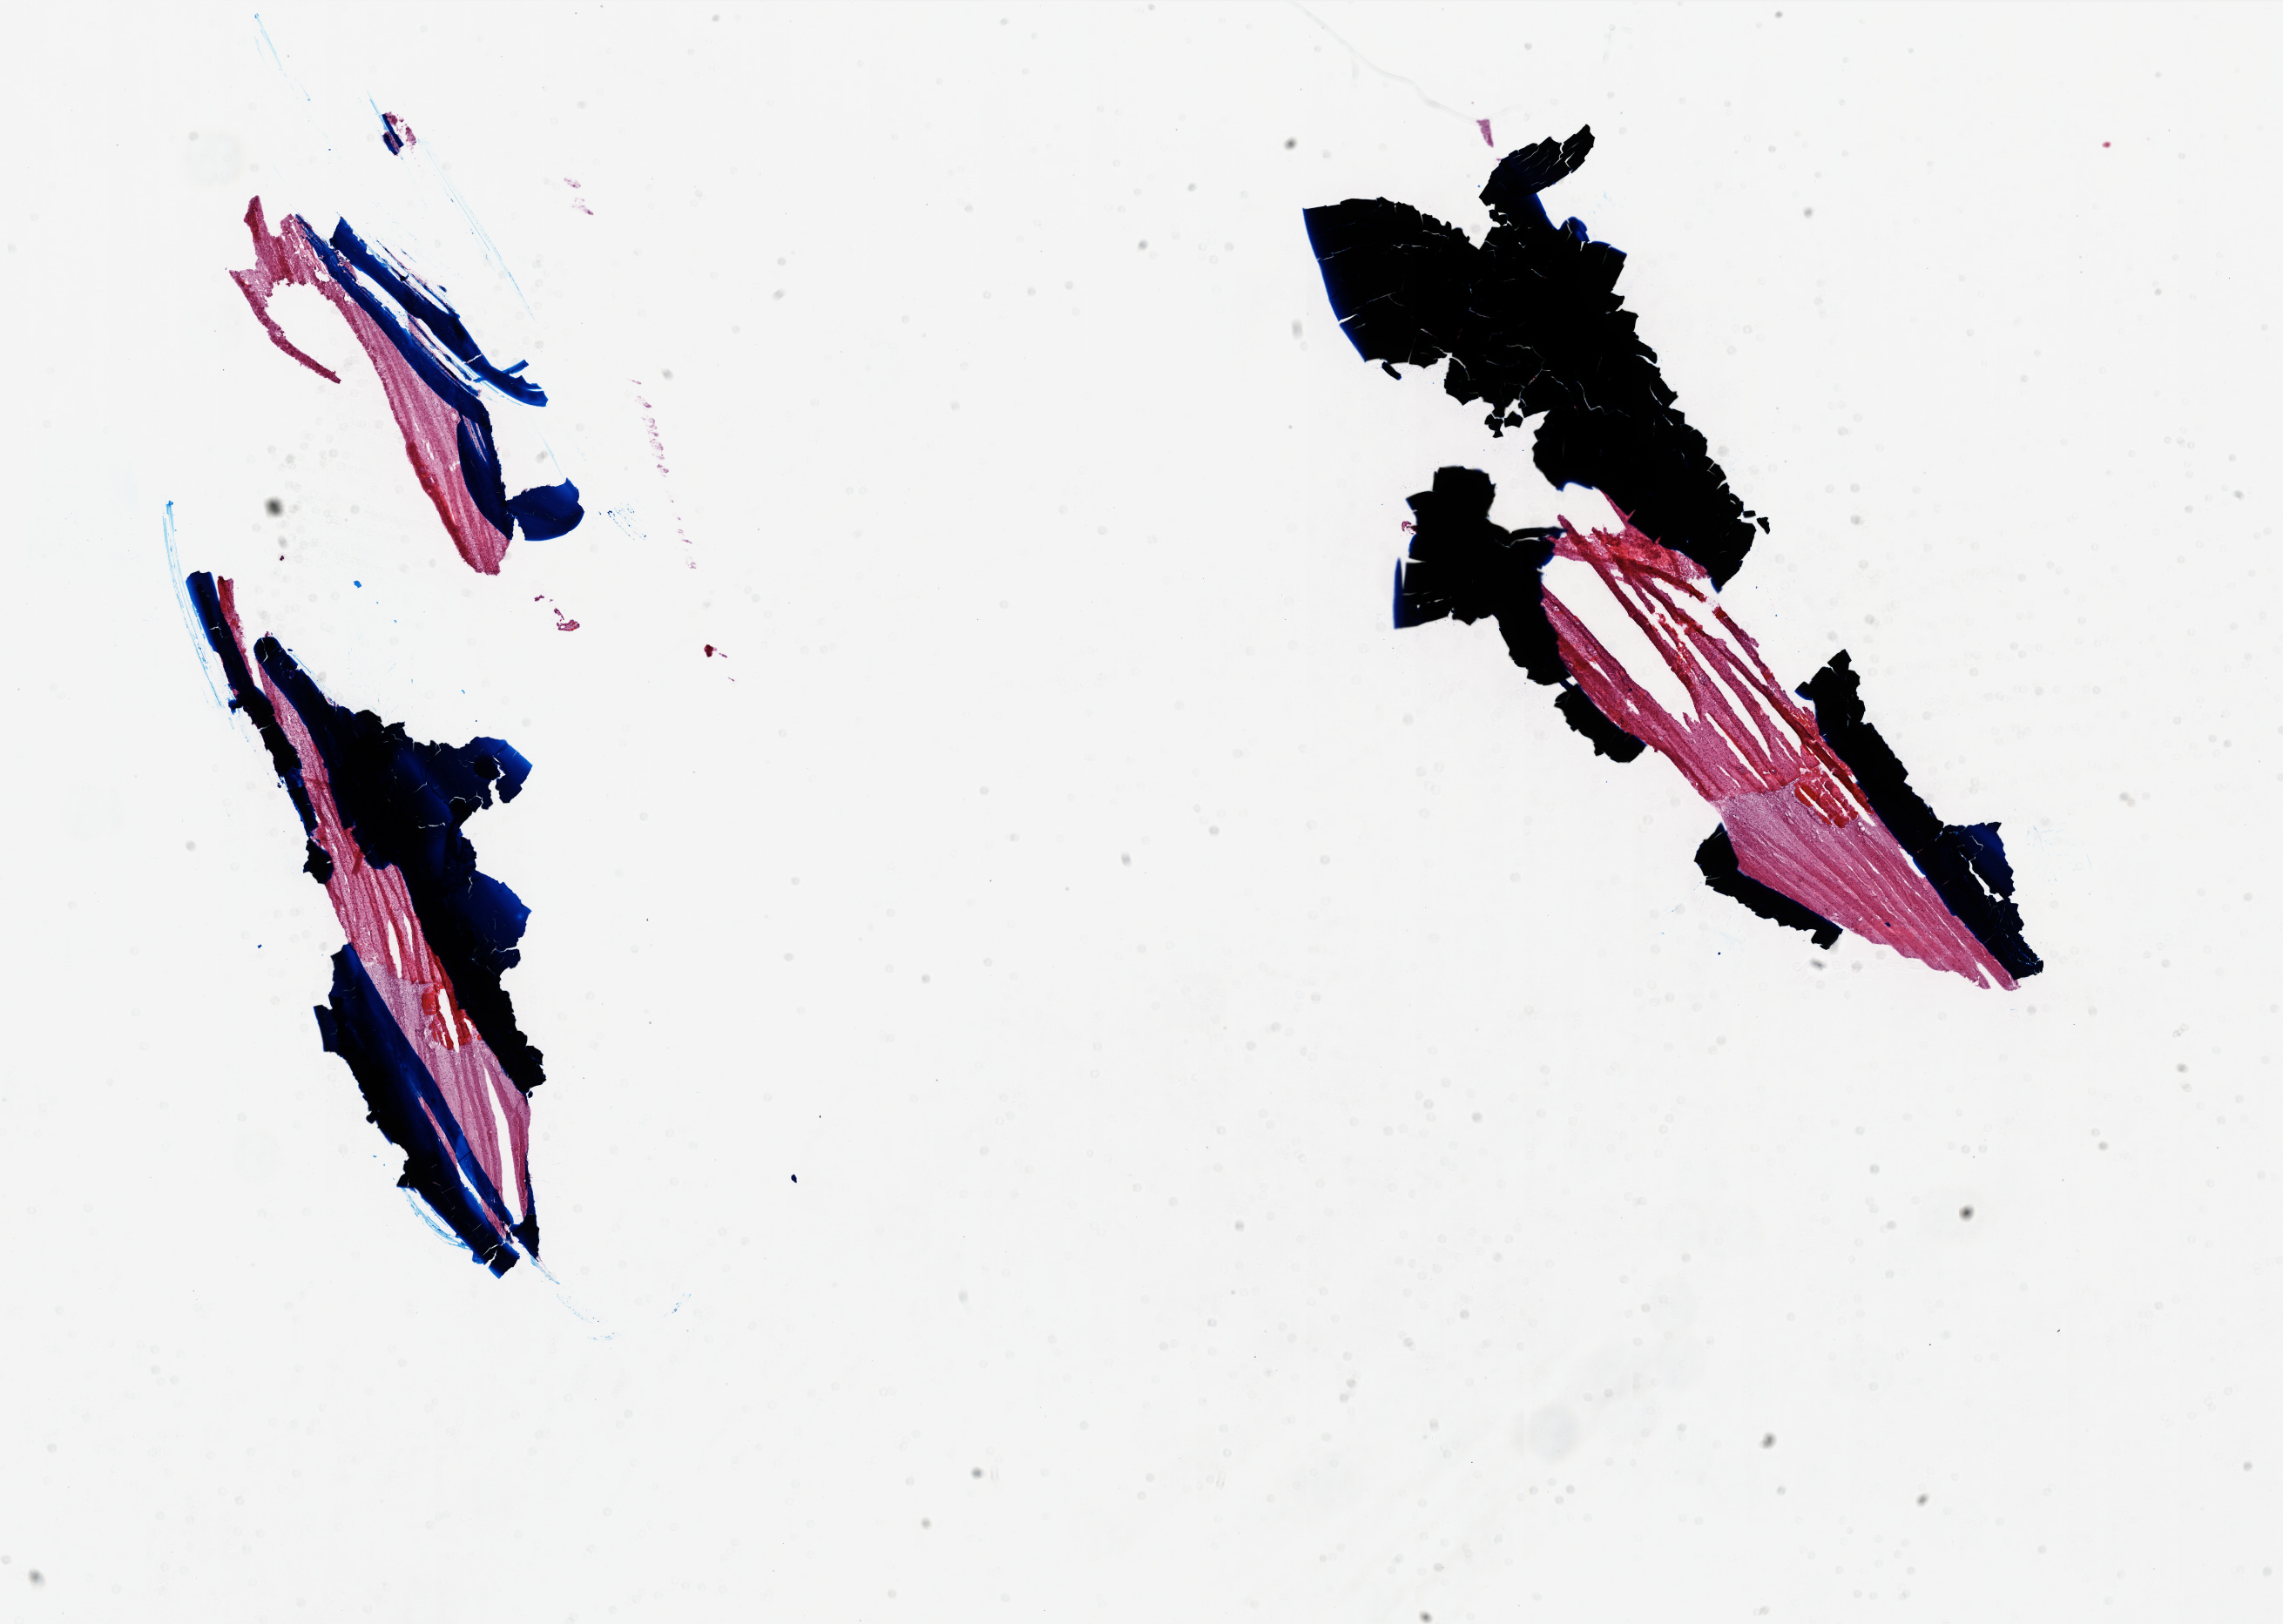
Digitized Hematoxylin and eosin (H&E) stained tissue section (whole slide) — whole scanned area (about 21.0 x 14.9 mm, slide scanned at 20x) shown as a low-resolution overview, frozen section from the top of the tissue portion, sample: primary tumour, brain. Male patient; age at initial diagnosis 69 years. Slide review estimates, as recorded: tumour cells 50%, tumour nuclei 90%, normal cells 0%, stromal cells 50%, necrosis 0%.
* diagnosis: Glioblastoma